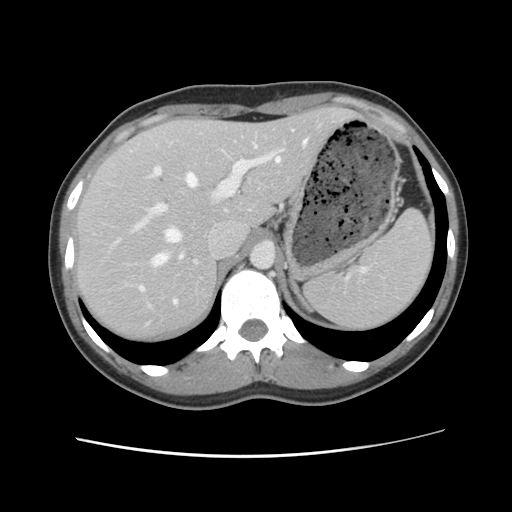
Contrast-enhanced abdominal CT, one axial slice; slice 81 of 134 in the series (ordered by position); intravenous contrast given; soft-tissue window (W 400 / L 40 HU); 512 × 512 image matrix, field of view 339 × 339 mm. Female patient, age 33 years. Case-level facts recorded for this patient, not image findings: diagnosis: colorectal cancer liver metastases, imaged before liver resection; multiple liver metastases: yes; largest metastasis: 4.5 cm; disease in both lobes: yes.
Structures marked on this image (outlined manually by an expert reader):
- hepatic veins: box from (x=143, y=139) to (x=307, y=305) px
- liver: (x=77, y=108)–(x=353, y=342)
- planned liver remnant (the part of the liver to remain after resection): (x=77, y=108)–(x=353, y=342)
- portal vein (with intrahepatic branches): (x=133, y=138)–(x=285, y=289)